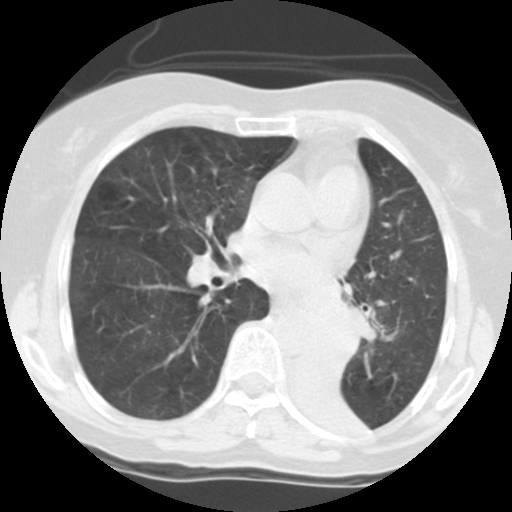
Low-dose screening chest CT, one axial slice; slice 66 of 113 in the series (ordered by position); 140 kVp; lung window (W 1500 / L -600 HU); 2.5 mm slice thickness; 512 × 512 image matrix, field of view 280 × 280 mm.
Outlined on this slice (outlined manually by an expert reader):
- lesion 1 (tumor, left main bronchus): bounding box <310,299,357,359> (left, top, right, bottom; pixels)